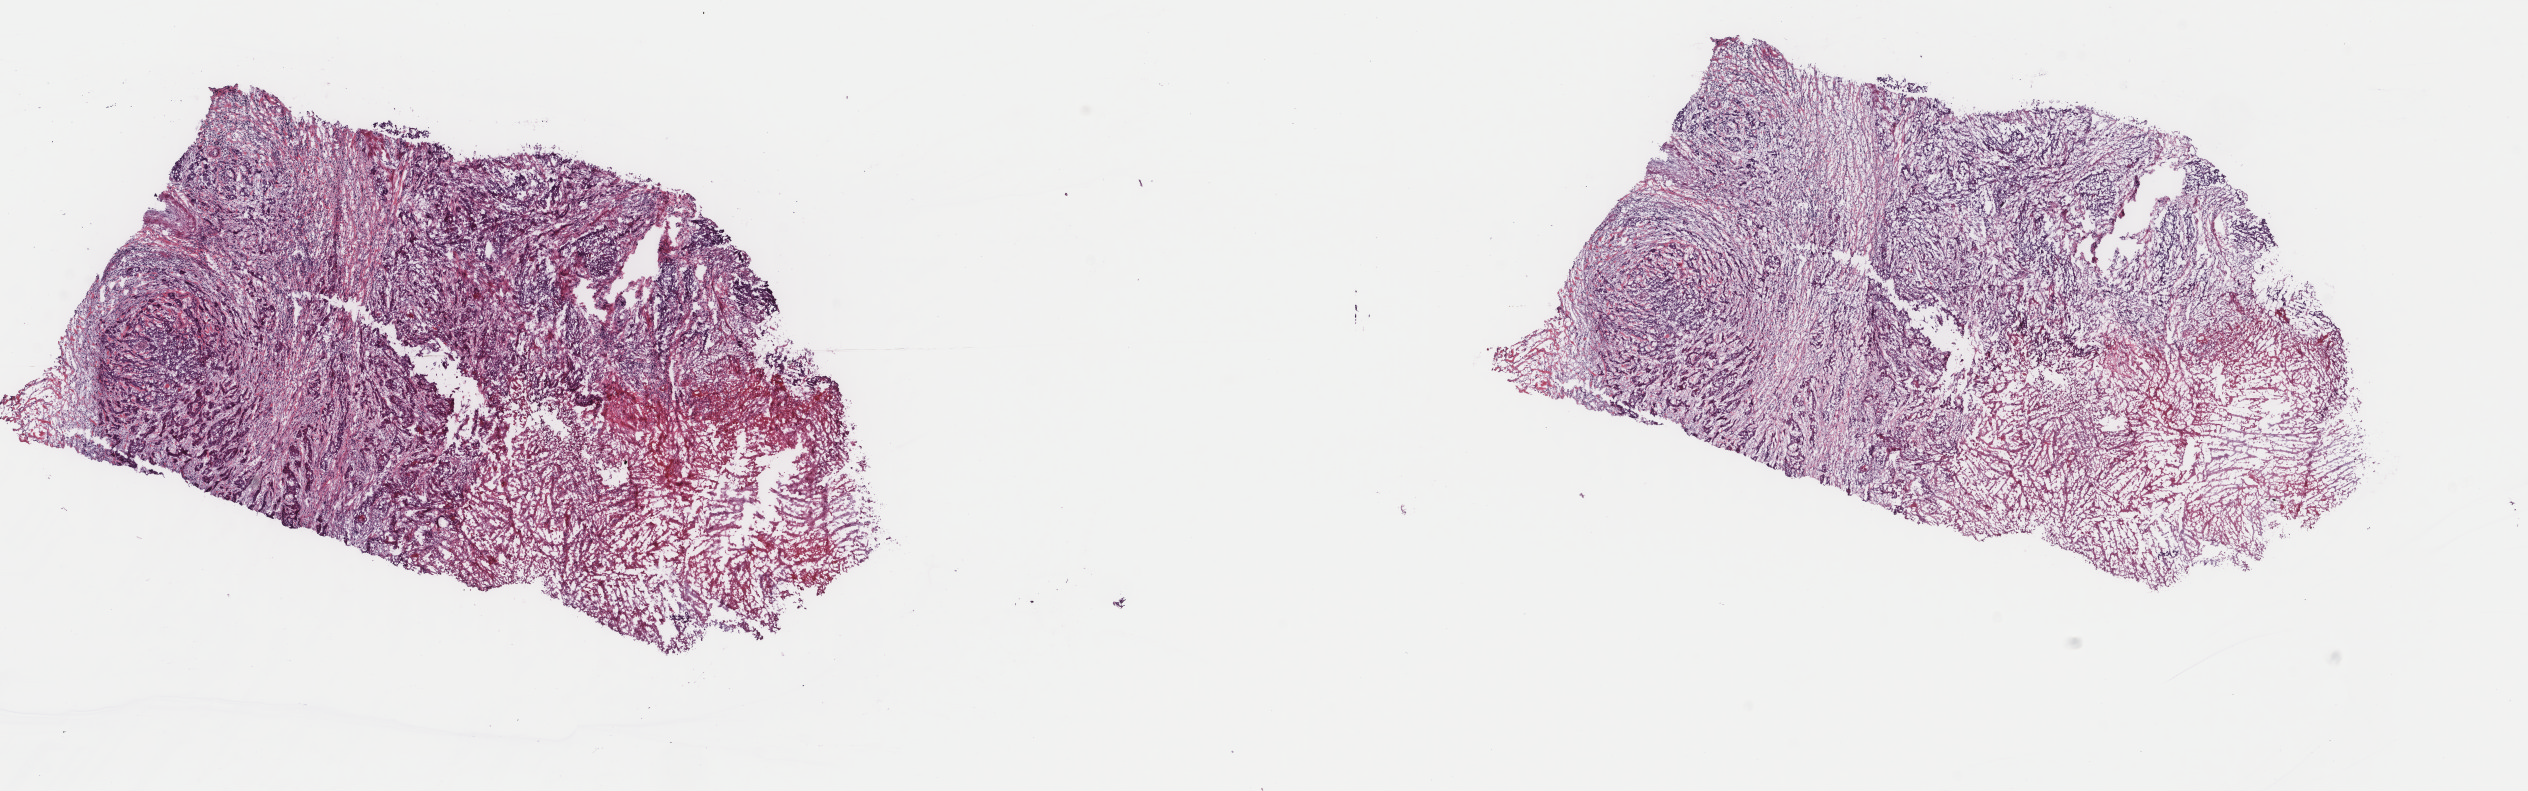
H&E-stained whole-slide image, whole scanned area (about 20.1 x 6.3 mm) shown as a low-resolution overview. Frozen section from the top of the tissue portion. Sample: primary tumour, esophagus. Patient: male, age at initial diagnosis 58 years. Histologic grade: G2 (moderately differentiated). Slide review estimates, as recorded: tumour cells 60%, tumour nuclei 60%, normal cells 0%, stromal cells 25%, necrosis 15%. Infiltration values recorded for this section: lymphocyte infiltration 3%, monocyte infiltration 2%, neutrophil infiltration 4%.
AJCC pathologic stage: IIIA (7th edition). Pathologic diagnosis: Squamous cell carcinoma, NOS (lower third of esophagus). Lymph nodes positive (case pathology): 1 of 1 examined.